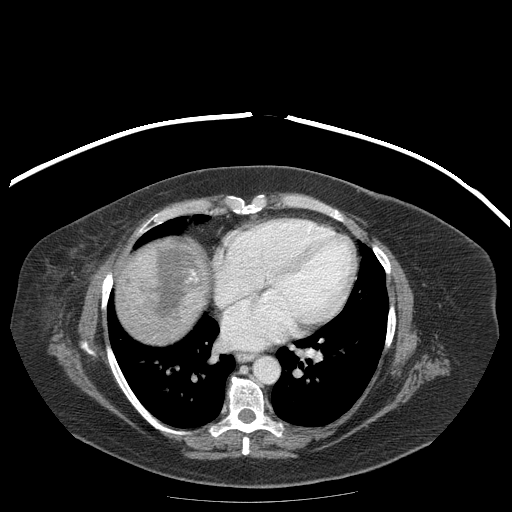
Contrast-enhanced abdominal CT (liver protocol), one axial slice; position 179 of 204 along the scan axis; reconstruction kernel STANDARD; soft-tissue window (W 400 / L 40 HU); 512 × 512 image matrix, field of view 440 × 440 mm. Case-level facts recorded for this patient, not image findings: diagnosis: hepatocellular carcinoma (patient treated with transarterial chemoembolisation; whether this scan precedes or follows treatment is not stated here); TNM stage (as recorded): Stage-IIIB; Child-Pugh class: A; tumour differentiation: well differentiated.
Annotated regions visible in this slice (semi-automatically segmented with operator editing):
- liver parenchyma outside the tumour (the mass and vessels are separate outlines, so this box may not span the whole liver): bounding box <116,238,206,344> (left, top, right, bottom; pixels)
- mass: <124,243,205,326>